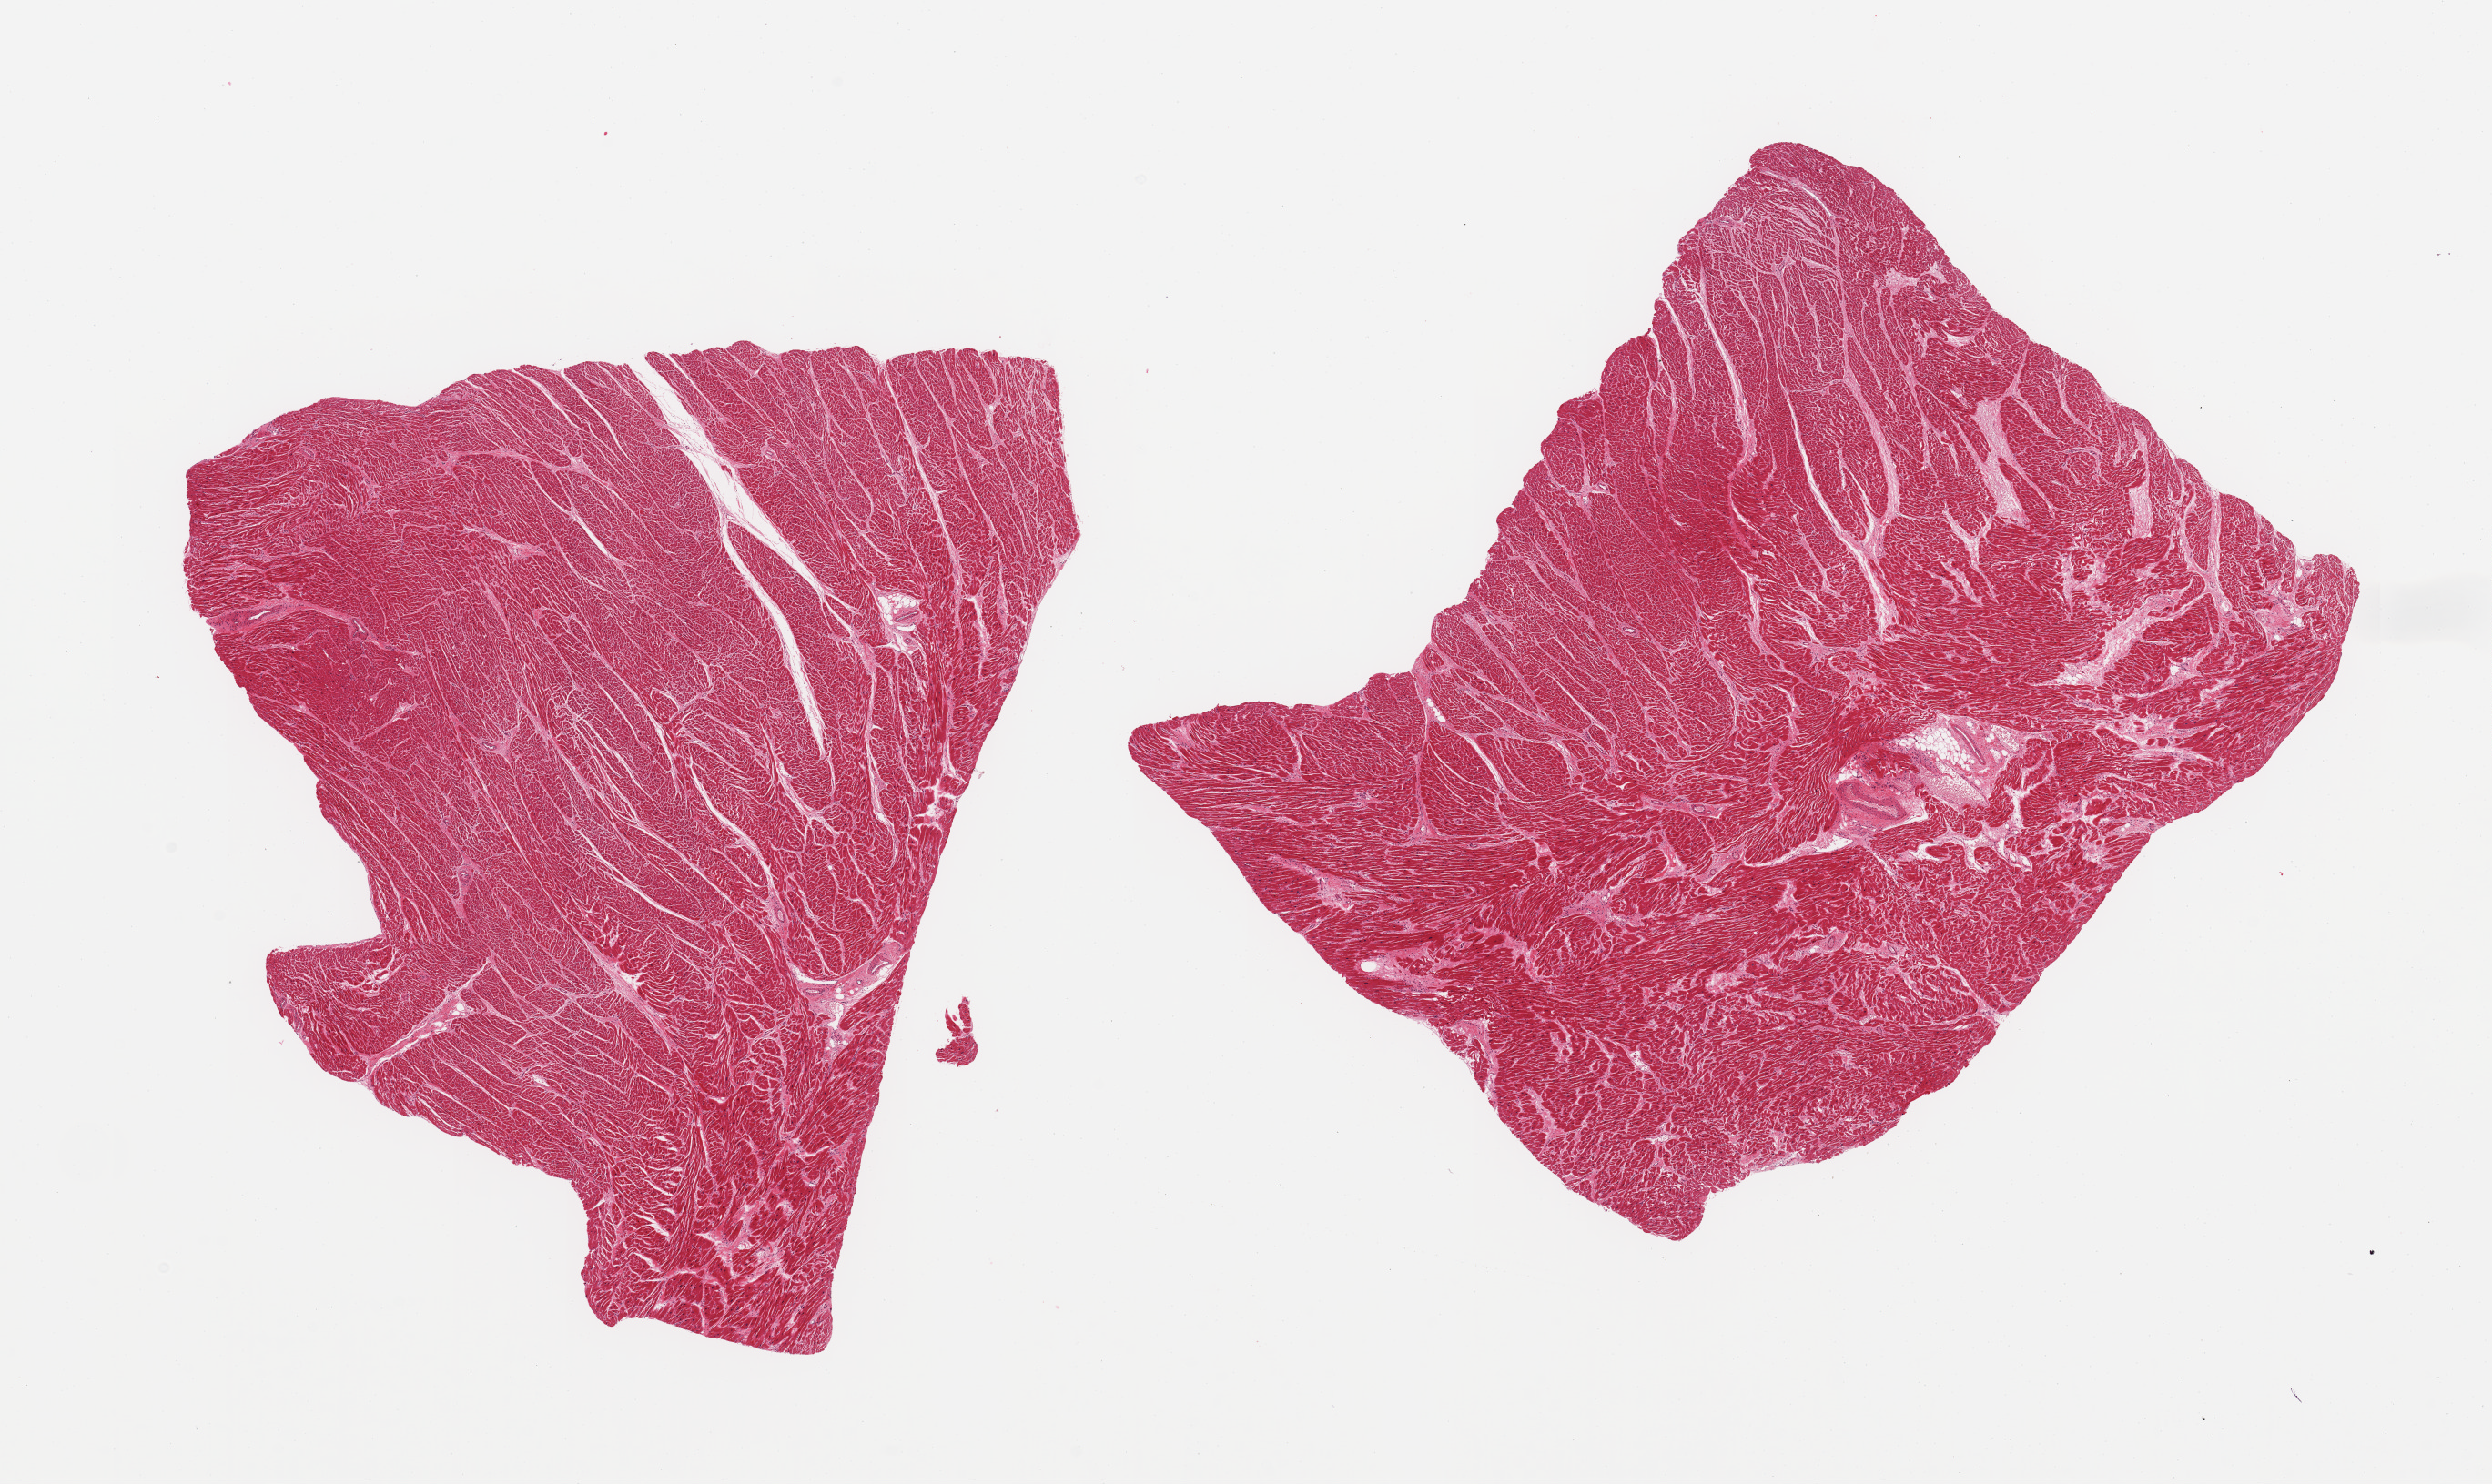
Digitized haematoxylin and eosin-stained section, a low-resolution overview of the entire scanned area, about 21.7 x 12.9 mm. PAXgene-fixed paraffin-embedded (PFPE) section. Section of heart (target tissue). Donor tissue sample.
• pathologist's review note for this sample: 2 pieces, no significant chronic ischemic changes